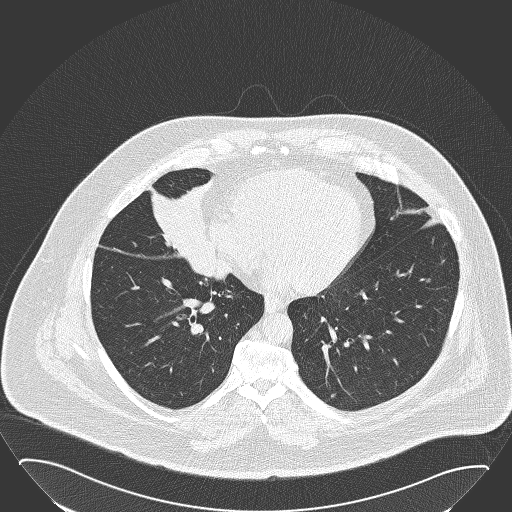
Low-dose screening chest CT, one axial slice. Slice 66 of 168 in the series (ordered by position). Reconstruction kernel B50f. 120 kVp. Lung window (W 1500 / L -600 HU). 2 mm slice thickness. 512 × 512 image matrix, field of view 432 × 432 mm.
Annotated regions visible in this slice (outlined manually by an expert reader):
- lesion 1 (tumor, hilum of right lung): bounding box (x1, y1, x2, y2) in pixels: (151, 178, 231, 280)